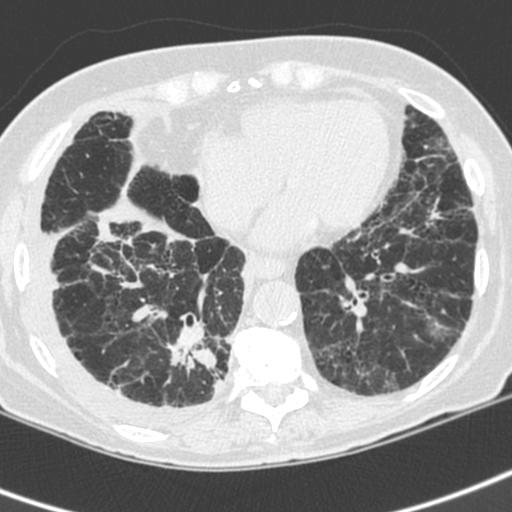
Axial slice from a low-dose chest CT screening exam, first (baseline) screen, lung window (W 1500 / L -600 HU), 1.3 mm slice thickness, 512 × 512 image matrix, field of view 288 × 288 mm. Female participant, aged 73 years at enrolment. Current smoker at enrolment.
Expert-annotated lung lesion, bounding box <154,315,234,406> (left, top, right, bottom; pixels). The exam's reader record, not a measurement of the box and not confirmed to be the same lesion: non-calcified nodule or mass ≥4 mm, right lower lobe, 35 × 30 mm, spiculated (stellate) margins, soft tissue attenuation. Official screen result: positive, change unspecified: nodule(s) >= 4 mm or enlarging nodule(s), mass(es), or other non-specific abnormalities suspicious for lung cancer. Lung cancer was diagnosed 22 days after this screen: adenocarcinoma, NOS, right lower lobe, stage IV (AJCC 6th edition), 35 mm at pathology.